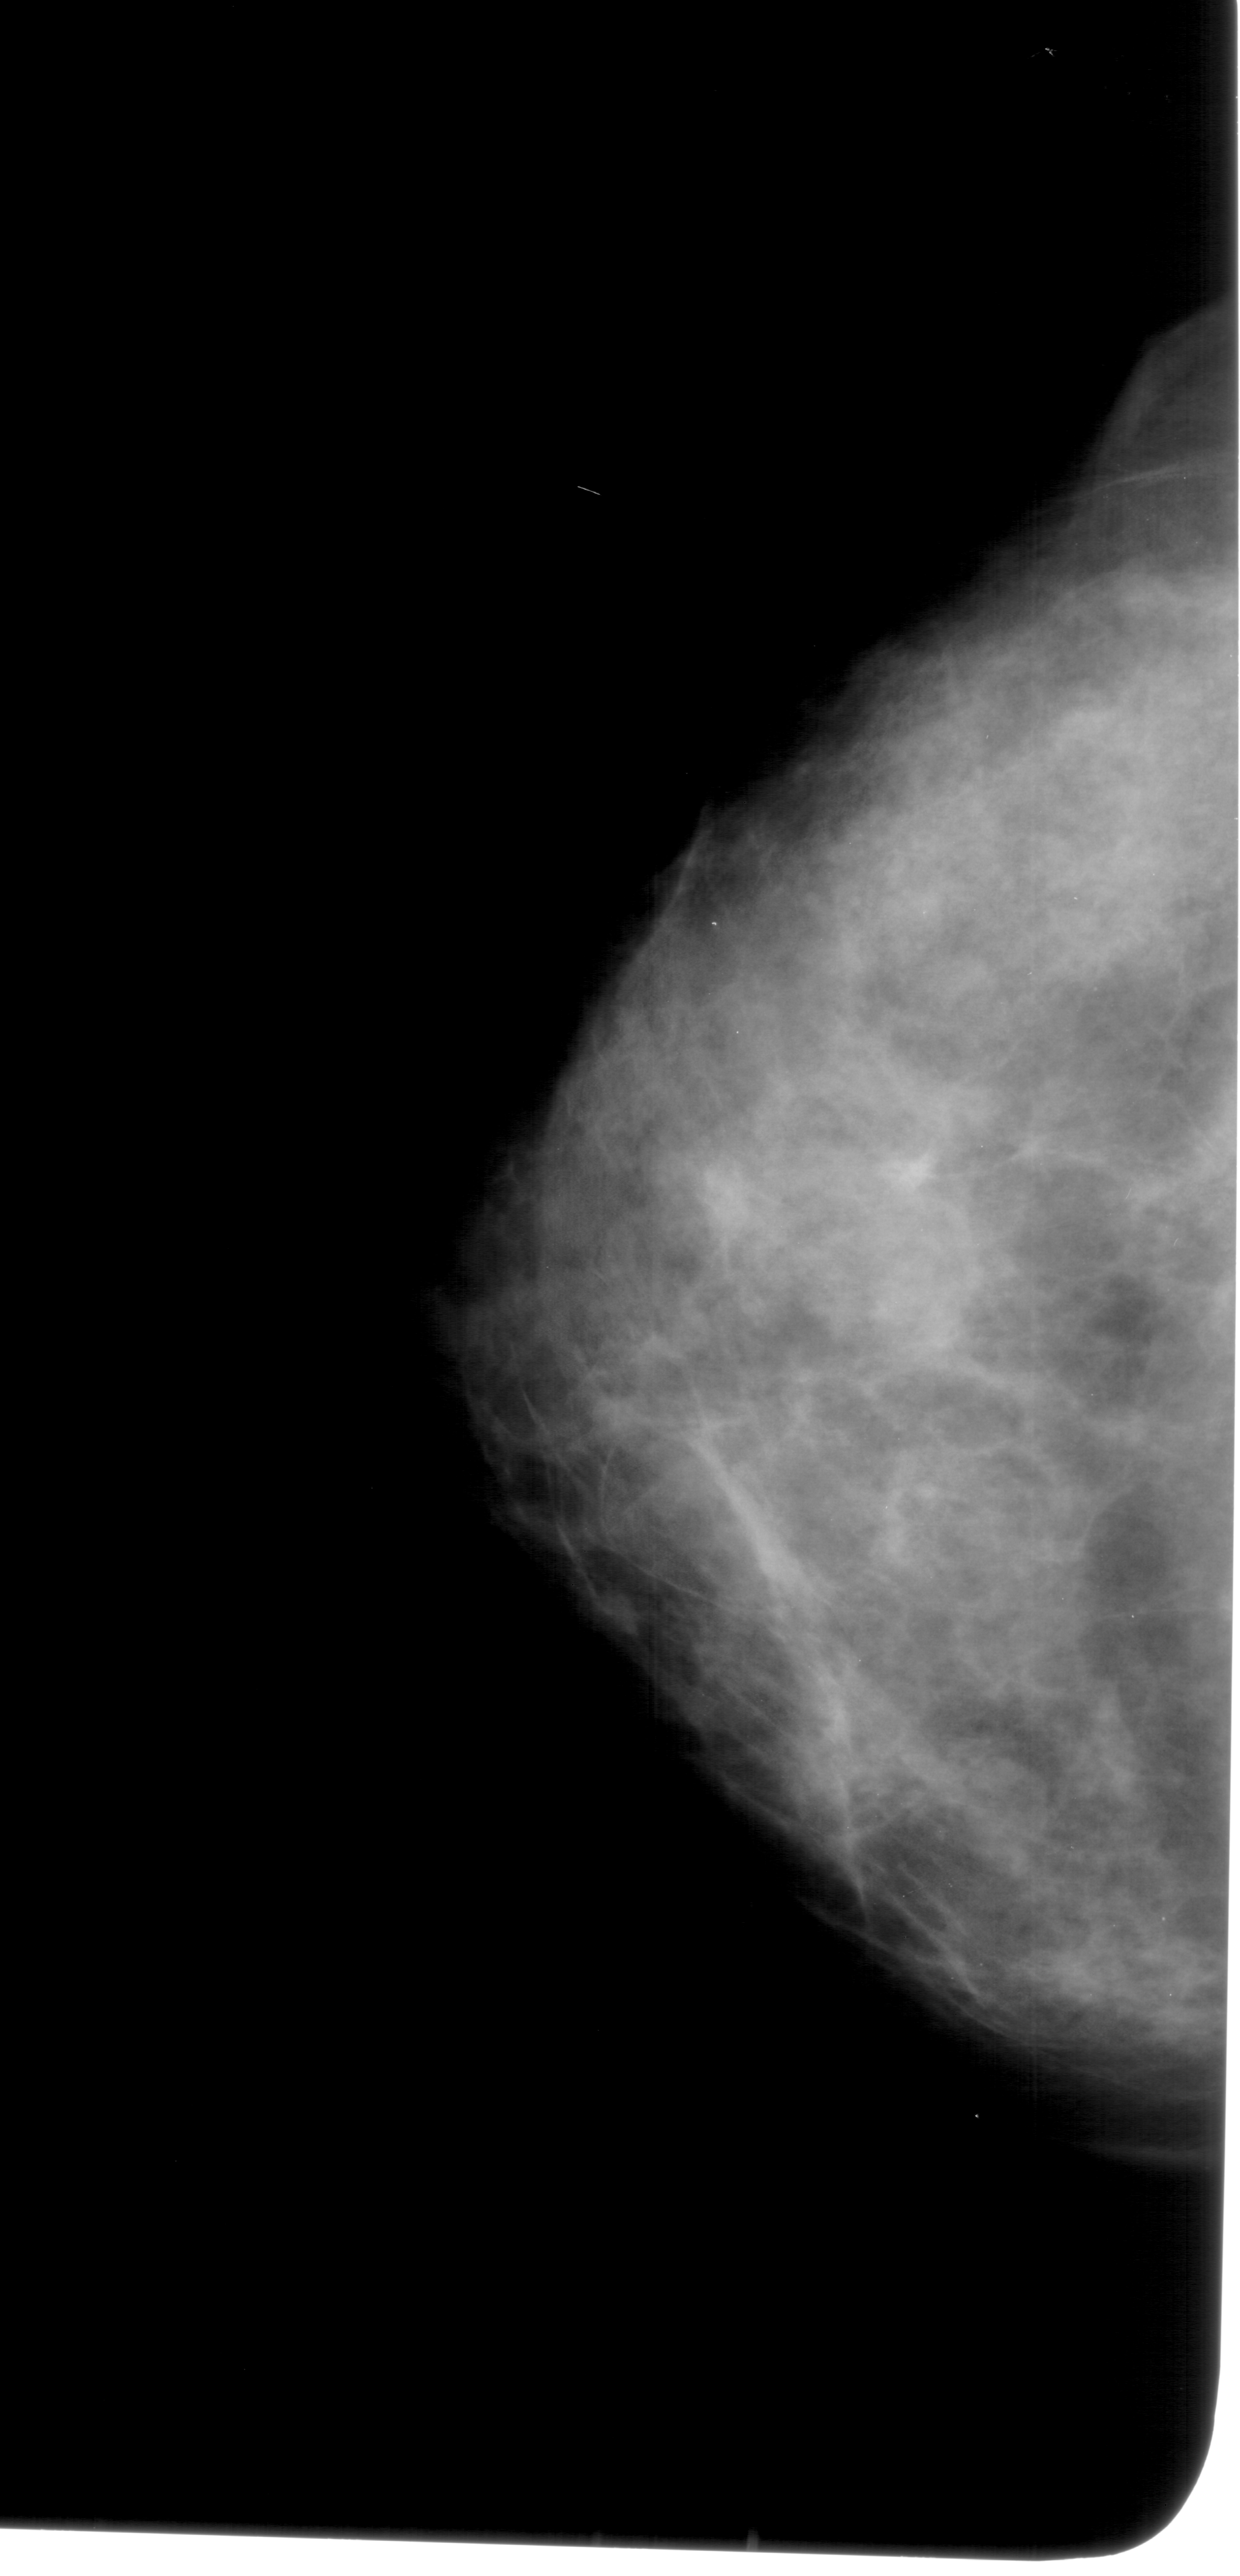
Mammogram (digitized film); left breast; CC view.
- Radiologist-marked abnormalities on this image: mass, shape round, margins circumscribed; BI-RADS assessment category 4; subtlety rating 3 on a 1 (subtle) to 5 (obvious) scale; pathology (as recorded): benign.